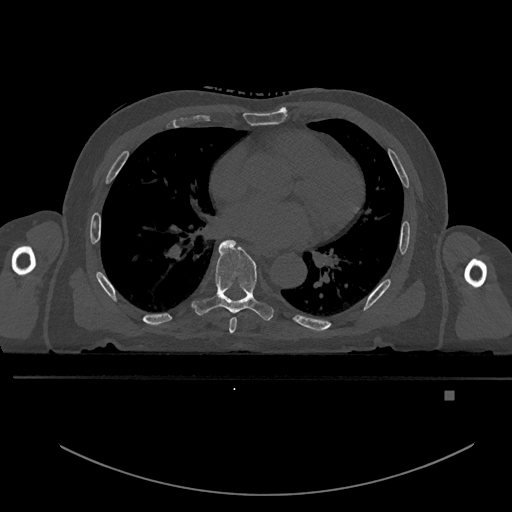
CT including the spine, one axial slice. Slice 259 of 969 in the series (ordered by position). Bone window (W 1800 / L 400 HU). 0.5 mm slice thickness. 512 × 512 image matrix, field of view 456 × 456 mm. Male patient, age 82 years. Case-level facts recorded for this patient, not image findings: primary cancer: prostate; vertebrae with lytic lesions (as recorded): T11, T9, T8, T2.
Annotated regions visible in this slice (semi-automatically segmented with operator editing):
- T6 vertebra: bounding box (x1, y1, x2, y2) in pixels: (229, 317, 237, 334)
- T7 vertebra: (192, 239, 273, 321)